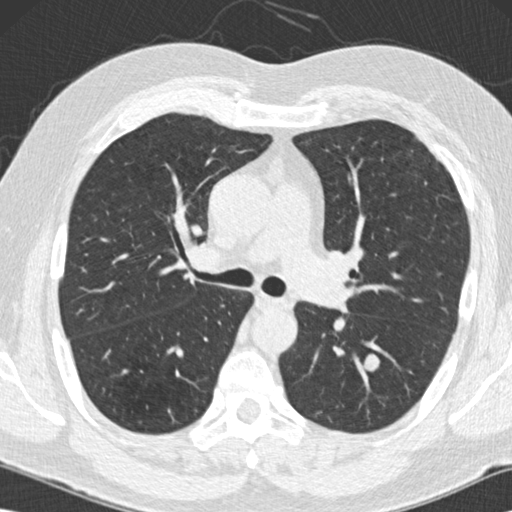
Low-dose screening chest CT, one axial slice. Slice 90 of 152 in the series (ordered by position). Lung window (W 1500 / L -600 HU). 512 × 512 image matrix, field of view 350 × 350 mm.
Annotated regions visible in this slice (outlined manually by an expert reader):
- lesion 2 (nodule, lower lobe of left lung): bounding box <364,354,380,371> (left, top, right, bottom; pixels)